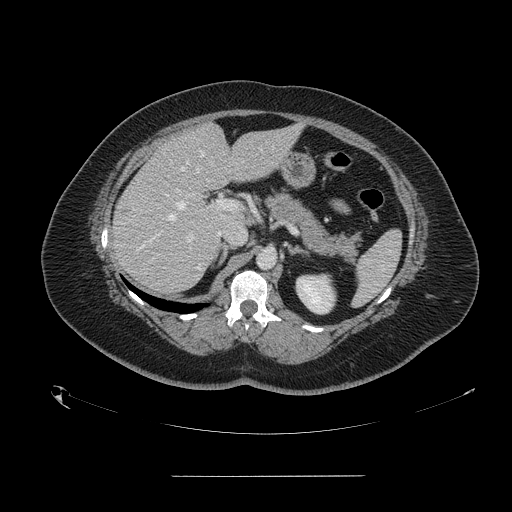
Contrast-enhanced abdominal CT, one axial slice. Position 91 of 164 along the scan axis. 120 kVp. Intravenous contrast given. Soft-tissue window (W 400 / L 40 HU). 2.5 mm slice thickness. 512 × 512 image matrix. Female patient, age 52 years. Case-level facts recorded for this patient, not image findings: diagnosis: colorectal cancer liver metastases, imaged before liver resection; multiple liver metastases: yes; largest metastasis: 3.5 cm; chemotherapy before resection: no.
Outlined on this slice (manually delineated by an expert):
- hepatic veins: bounding box <150,151,204,242> (left, top, right, bottom; pixels)
- liver: <113,124,299,292>
- planned liver remnant (the part of the liver to remain after resection): <176,124,299,226>
- portal vein (with intrahepatic branches): <176,189,239,241>
- liver metastasis: <123,211,128,213>